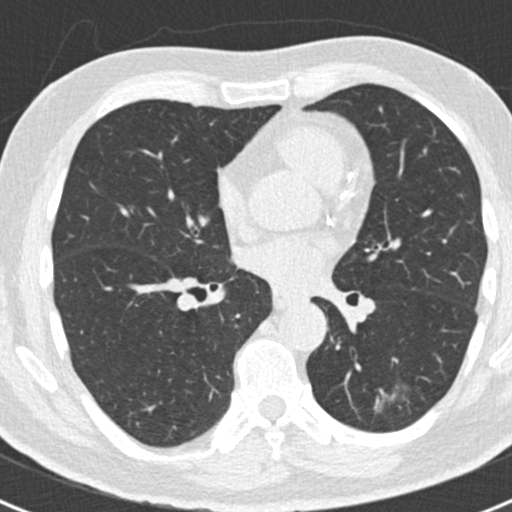
Low-dose screening chest CT, axial slice; first (baseline) screen; lung window (W 1500 / L -600 HU); 2 mm slice thickness; slice 88 of 188 in the series. Male participant, aged 66 years at enrolment. Former smoker at enrolment.
• Lesion marked by an expert reader, bounding box (x1, y1, x2, y2) in pixels: (348, 344, 422, 424).
• The exam's reader record, not a measurement of the box and not confirmed to be the same lesion: non-calcified nodule or mass ≥4 mm, left lower lobe, 43 × 27 mm, smooth margins.
• Lung cancer was diagnosed 801 days after this screen (after the third annual screen): adenocarcinoma, NOS, left lower lobe, poorly differentiated (G3), stage IB (AJCC 6th edition), 38 mm at pathology.